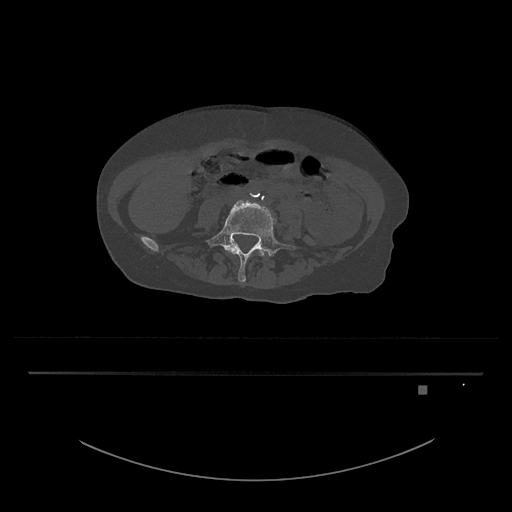
CT including the spine, one axial slice. Position 314 of 797 along the scan axis. Reconstruction kernel Br40s/3. 120 kVp. Bone window (W 1800 / L 400 HU). 0.5 mm slice thickness. 512 × 512 image matrix, field of view 500 × 500 mm. Female patient, age 57 years. Case-level facts recorded for this patient, not image findings: primary cancer: cervical.
Outlined on this slice (semi-automatic segmentation, software-assisted and operator-edited):
- L4 vertebra: bounding box <229,244,271,257> (left, top, right, bottom; pixels)